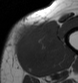
MRI of an extremity soft-tissue mass, one axial slice; position 11 of 43 along the scan axis; MR volume resampled by the dataset authors to the PET/CT grid (not the native acquisition matrix); 3.27 mm slice thickness; 78 × 83 image matrix. Male patient. Case-level facts recorded for this patient, not image findings: histological type: pleiomorphic leiomyosarcoma; grade: high; site of the primary tumour: left thigh.
Annotated regions visible in this slice (expert contour drawn on MRI and transferred to this co-registered scan by the dataset authors):
- gross tumour volume including surrounding oedema: bounding box <15,21,58,70> (left, top, right, bottom; pixels)
- gross tumour volume (mass): <15,21,55,63>